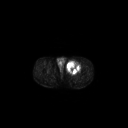
FDG PET of an extremity soft-tissue mass (from a PET/CT study), one axial slice; position 256 of 267 along the scan axis; 3.27 mm slice thickness; 128 × 128 image matrix, field of view 700 × 700 mm. Patient: male, 63 years. From the clinical record (not read from this slice): histological type: pleiomorphic liposarcoma; grade: high; site of the primary tumour: left thigh.
Structures marked on this image (expert contour drawn on MRI and transferred to this co-registered scan by the dataset authors):
- gross tumour volume including surrounding oedema: bounding box <66,60,81,73> (left, top, right, bottom; pixels)
- gross tumour volume (mass): <66,61,80,73>